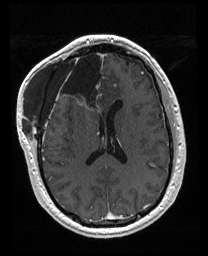
Brain MRI from a brain-tumour surgery series, one axial slice. Slice 79 of 176 in the series (ordered by position). T1-weighted post-contrast. 208 × 256 image matrix, field of view 208 × 256 mm. Case-level facts recorded for this patient, not image findings: histopathology: Astrocytoma; WHO grade: 4; IDH mutation: yes; tumour location: Right Orbitofrontal Anterior Temporal Insular.
Outlined on this slice (expert manual segmentation):
- previous resection cavity: bounding box <56,52,106,111> (left, top, right, bottom; pixels)